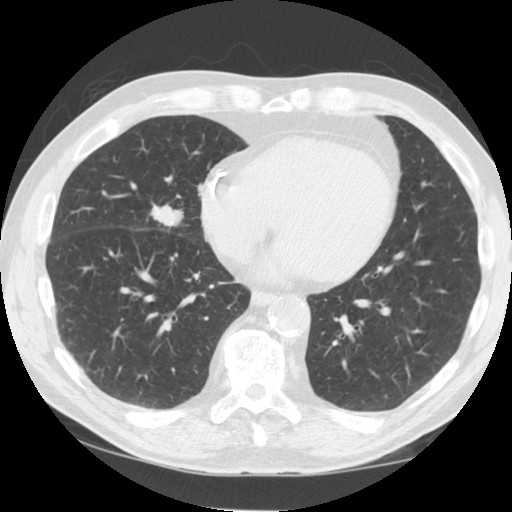
Low-dose screening chest CT, axial slice; third screening round (two years after baseline); lung window (W 1500 / L -600 HU); slice 85 of 125 in the series. Male, age 64 years at enrolment. Current smoker at enrolment.
Expert-annotated lung lesion, bounding box [x1, y1, x2, y2] px = [131, 190, 202, 244]. Reader record for this screening exam (exam-level; its link to the box is not recorded): non-calcified nodule or mass ≥4 mm, right middle lobe, 21 × 14 mm, smooth margins, soft tissue attenuation, pre-existing on the prior screen: yes; interval growth: yes. Official screen result: positive, other. Participant outcome: lung cancer diagnosed 74 days after this screen — non-small cell carcinoma, right middle lobe, poorly differentiated (G3), stage IIIA (AJCC 6th edition), 20 mm at pathology.